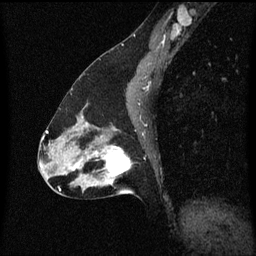
Breast MRI (dynamic contrast-enhanced), one sagittal slice; slice 32 of 60 in the series (ordered by position); dynamic contrast-enhanced series, image 2 of 3 at this slice position (ordered by acquisition); 1.5 T; TE 4.2 ms, TR 8.4 ms; 256 × 256 image matrix, field of view 200 × 200 mm. Female patient, age 47 years.
Annotated regions visible in this slice (semi-automatically segmented with operator editing):
- analysis volume of interest (the breast-tissue region the enhancement analysis was run in; not a lesion): bounding box <85,136,136,197> (left, top, right, bottom; pixels)
- tumour enhancement mask (voxels above the 70 % enhancement threshold inside the analysis volume of interest): <93,146,131,183>